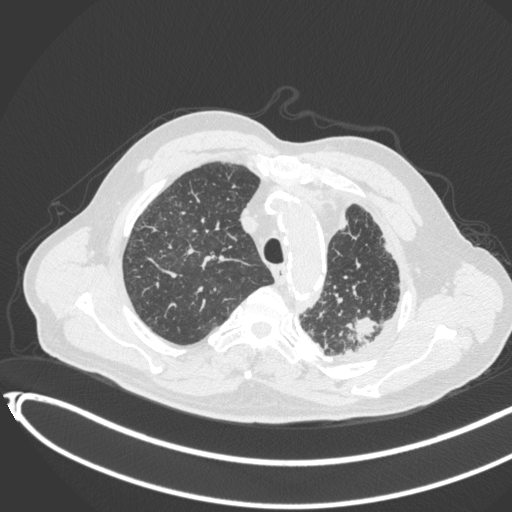
Chest CT, one axial slice. Position 339 of 451 along the scan axis. 120 kVp. Lung window (W 1500 / L -600 HU). 1 mm slice thickness. 512 × 512 image matrix, field of view 400 × 400 mm. Patient: male, 78 years. Case-level facts recorded for this patient, not image findings: clinical TNM (as recorded): T1c N0 M1.
Annotated regions visible in this slice (bounding box drawn by a radiologist):
- lung tumour (recorded histology: adenocarcinoma): bounding box (x1, y1, x2, y2) in pixels: (347, 314, 383, 346)